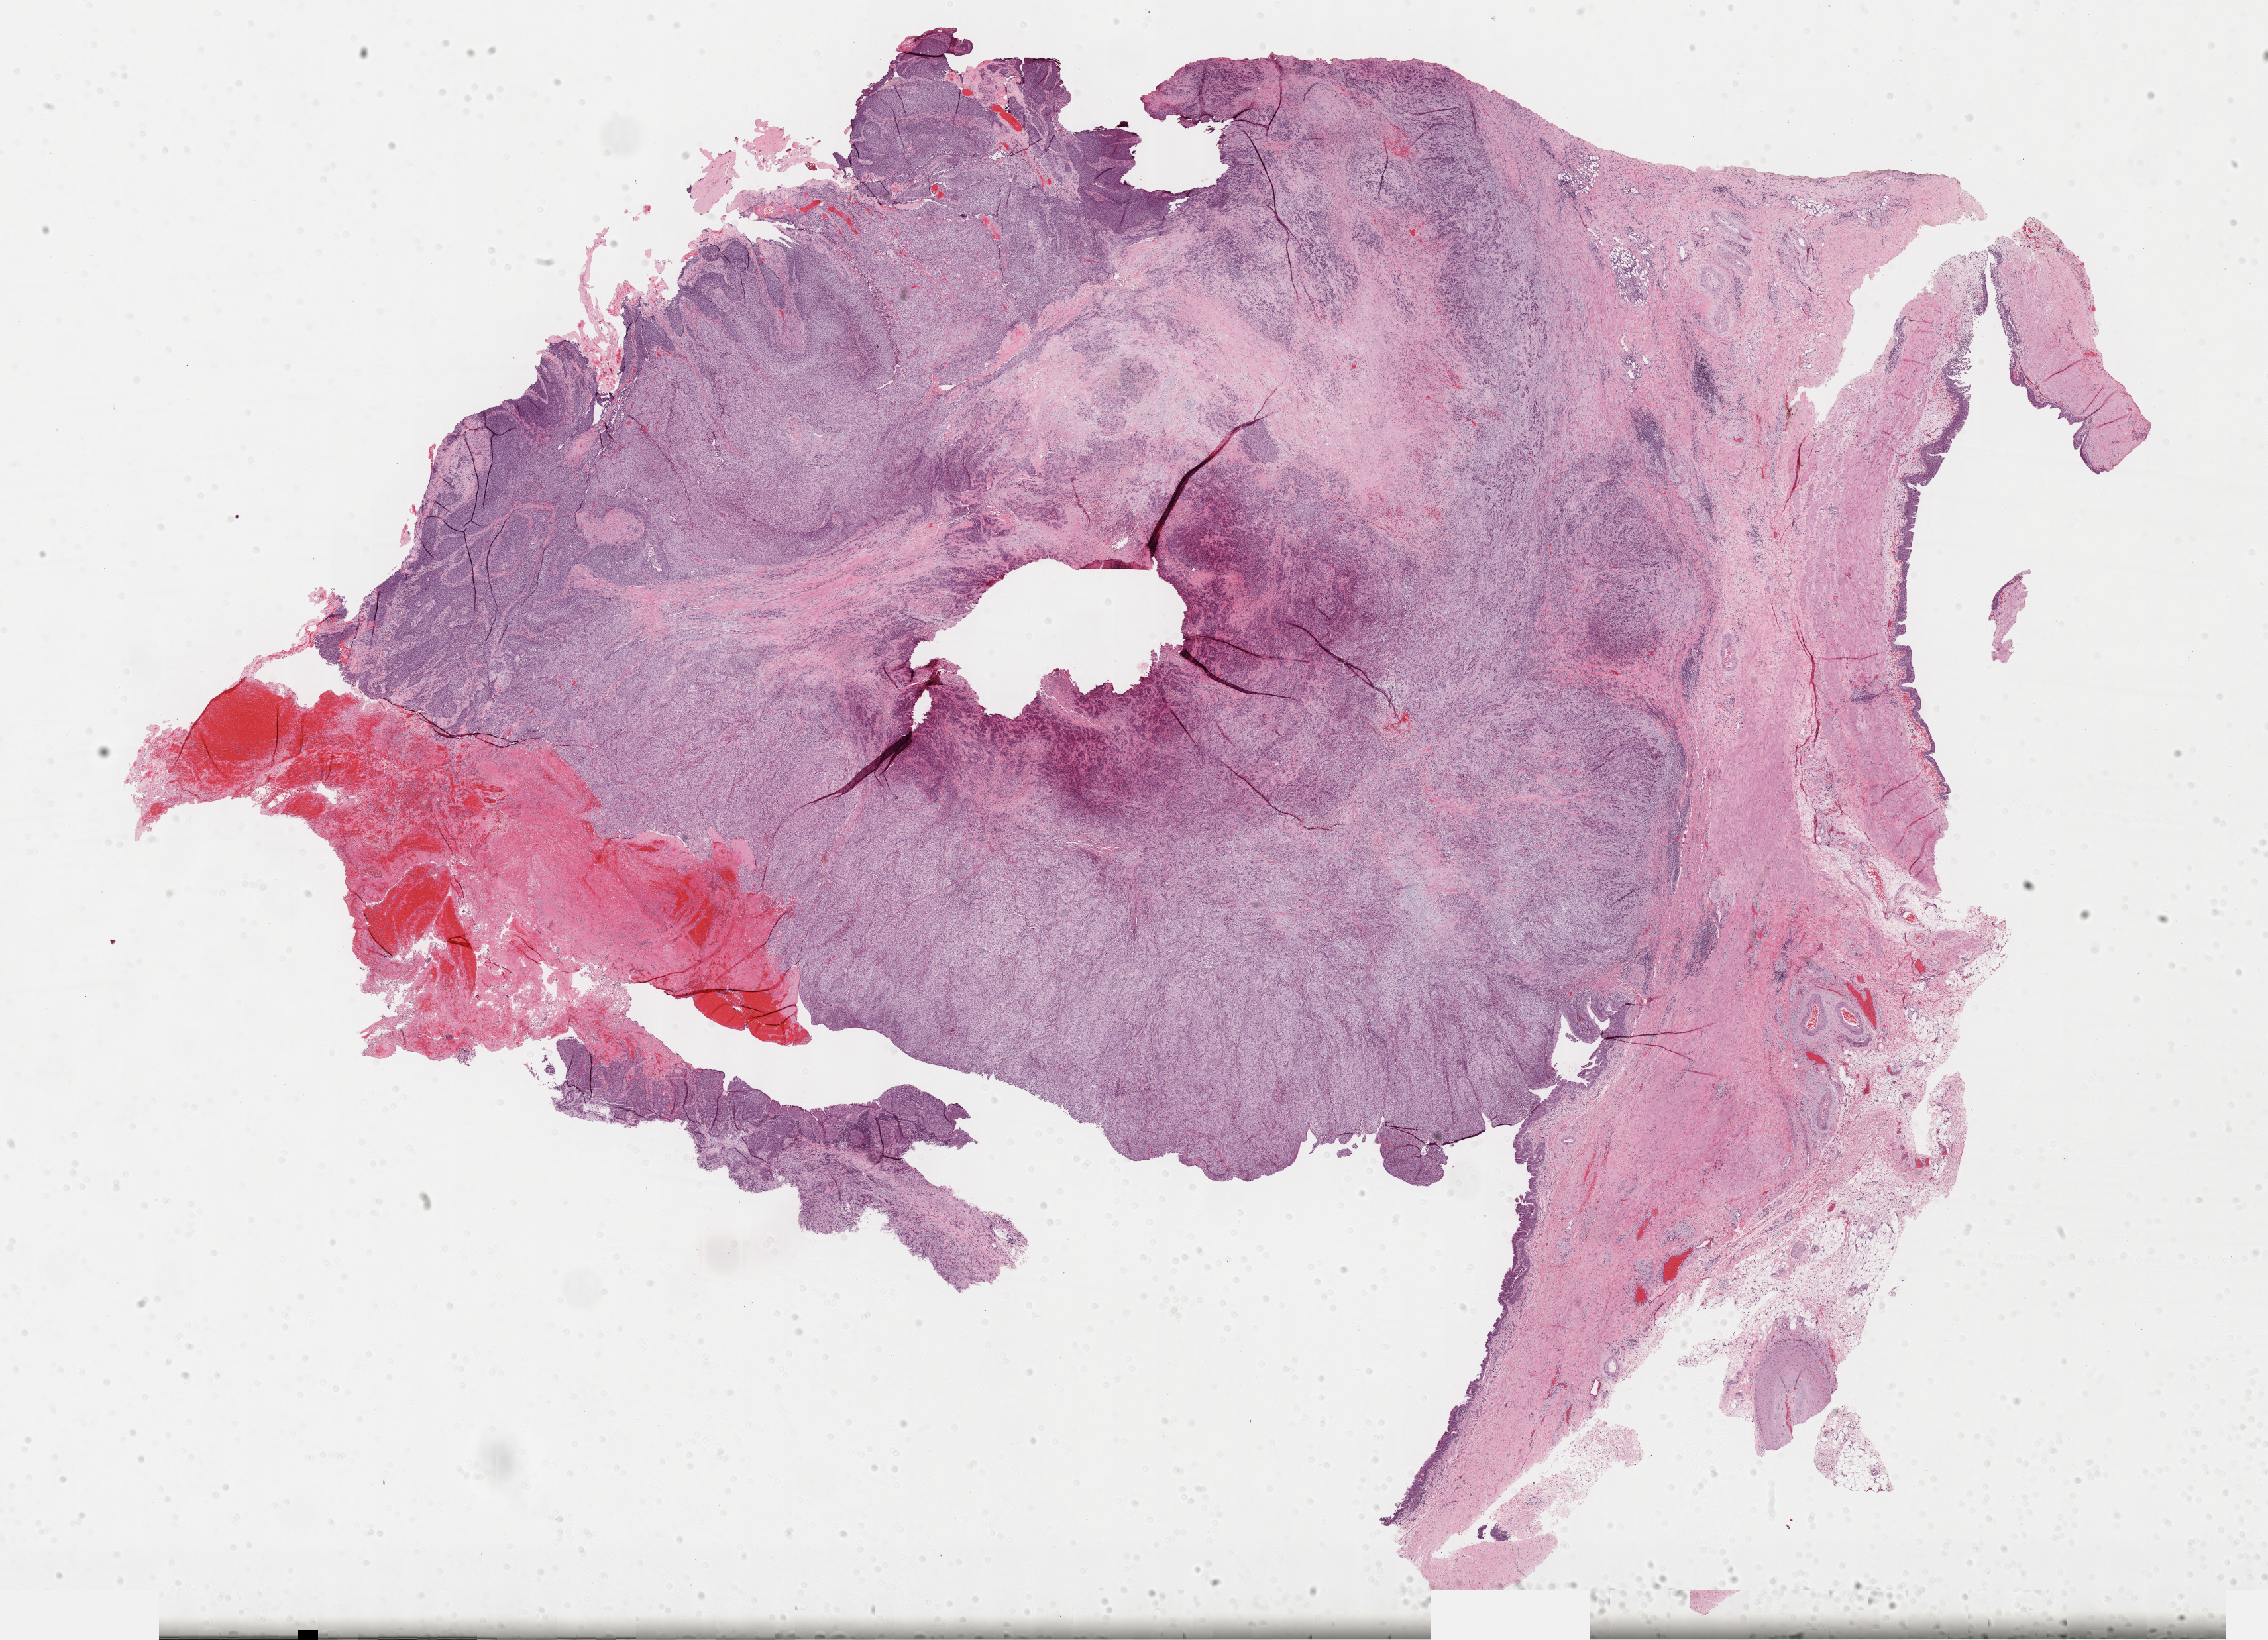
H&E-stained whole-slide image — low-resolution overview of the scanned area, about 27.7 x 20.0 mm (slide scanned at 40x), FFPE section, kidney, primary tumour sample. Female, age 68 years at initial diagnosis. Histologic grade: G2 (moderately differentiated).
AJCC pathologic stage: I (7th edition). Laterality: right. Diagnosis: Clear cell adenocarcinoma, NOS.